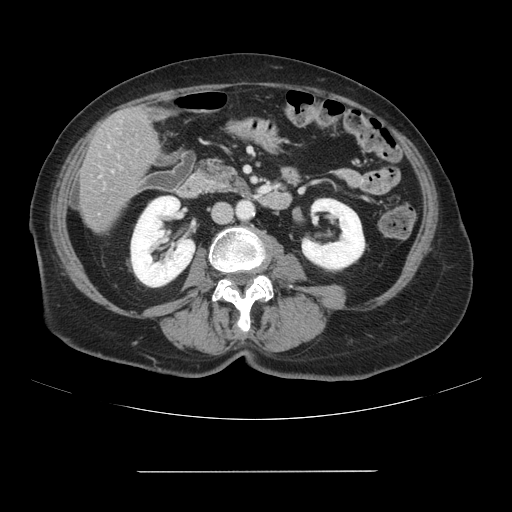
Contrast-enhanced abdominal CT, one axial slice. Slice 18 of 111 in the series (ordered by position). Intravenous contrast given. Soft-tissue window (W 400 / L 40 HU). 2.5 mm slice thickness. 512 × 512 image matrix, field of view 400 × 400 mm. Female patient, age 74 years. Case-level facts recorded for this patient, not image findings: diagnosis: colorectal cancer liver metastases, imaged before liver resection; multiple liver metastases: yes.
Outlined on this slice (manually delineated by an expert):
- liver: bounding box [x1, y1, x2, y2] px = [80, 106, 161, 233]